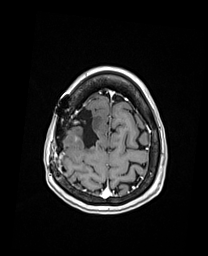
Brain MRI from a brain-tumour surgery series, one axial slice; slice 38 of 192 in the series (ordered by position); T1-weighted post-contrast; 1 mm slice thickness; 208 × 256 image matrix, field of view 208 × 256 mm. From the clinical record (not read from this slice): histopathology: Oligodendroglioma; WHO grade: 3; IDH mutation: yes; tumour location: Right Frontal.
Outlined on this slice (manually delineated by an expert):
- previous resection cavity: bounding box [x1, y1, x2, y2] px = [72, 109, 99, 148]